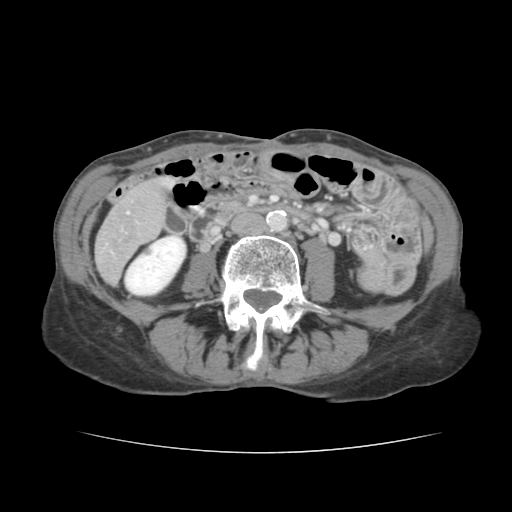
Contrast-enhanced abdominal CT, one axial slice. Position 28 of 136 along the scan axis. Intravenous contrast given. Soft-tissue window (W 400 / L 40 HU). 2.5 mm slice thickness. 512 × 512 image matrix. Female patient, age 77 years. Case-level facts recorded for this patient, not image findings: diagnosis: colorectal cancer liver metastases, imaged before liver resection; multiple liver metastases: yes; largest metastasis: 3 cm; disease in both lobes: no.
Structures marked on this image (outlined manually by an expert reader):
- liver: bounding box <96,180,169,282> (left, top, right, bottom; pixels)